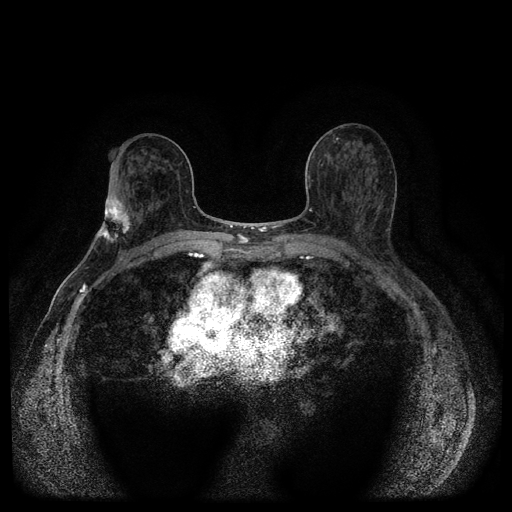
Breast MRI (dynamic contrast-enhanced, multi-phase), one axial slice; position 57 of 116 along the scan axis; dynamic contrast-enhanced series, time point 2 of 5 at this slice position (early post-contrast); 1.5 T; TE 2.7 ms, TR 5.4 ms; 512 × 512 image matrix. Female patient, age 75 years.
Outlined on this slice (semi-automatically segmented with operator editing):
- breast lesion (labelled 'tumour' in the annotation; benign lesions carry a separate 'benign' label): bounding box [x1, y1, x2, y2] px = [95, 194, 132, 244]